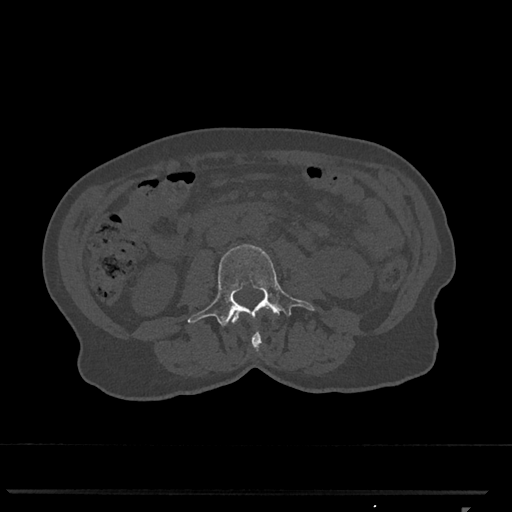
CT including the spine, one axial slice; position 284 of 793 along the scan axis; reconstruction kernel Br40s/3; 120 kVp; bone window (W 1800 / L 400 HU); 512 × 512 image matrix, field of view 380 × 380 mm. Female patient, age 62 years. From the clinical record (not read from this slice): primary cancer: renal.
Outlined on this slice (semi-automatic segmentation, software-assisted and operator-edited):
- L2 vertebra: bounding box <232,308,268,352> (left, top, right, bottom; pixels)
- L3 vertebra: <187,244,315,327>